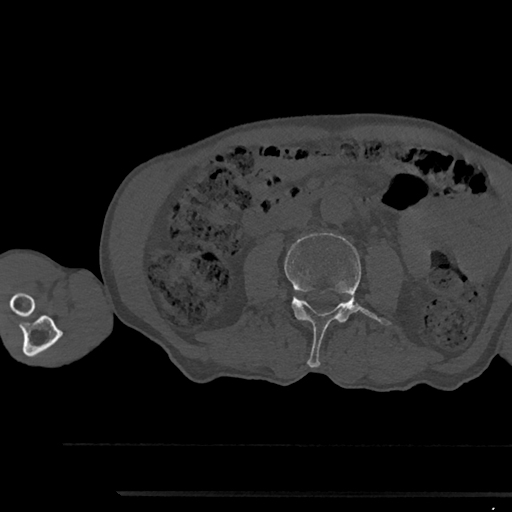
CT including the spine, one axial slice. Slice 484 of 797 in the series (ordered by position). Reconstruction kernel Br40s/3. 120 kVp. Bone window (W 1800 / L 400 HU). 0.5 mm slice thickness. 512 × 512 image matrix. Male patient, age 79 years. Case-level facts recorded for this patient, not image findings: primary cancer: prostate.
Structures marked on this image (semi-automatically segmented with operator editing):
- L3 vertebra: box from (x=284, y=233) to (x=390, y=367) px